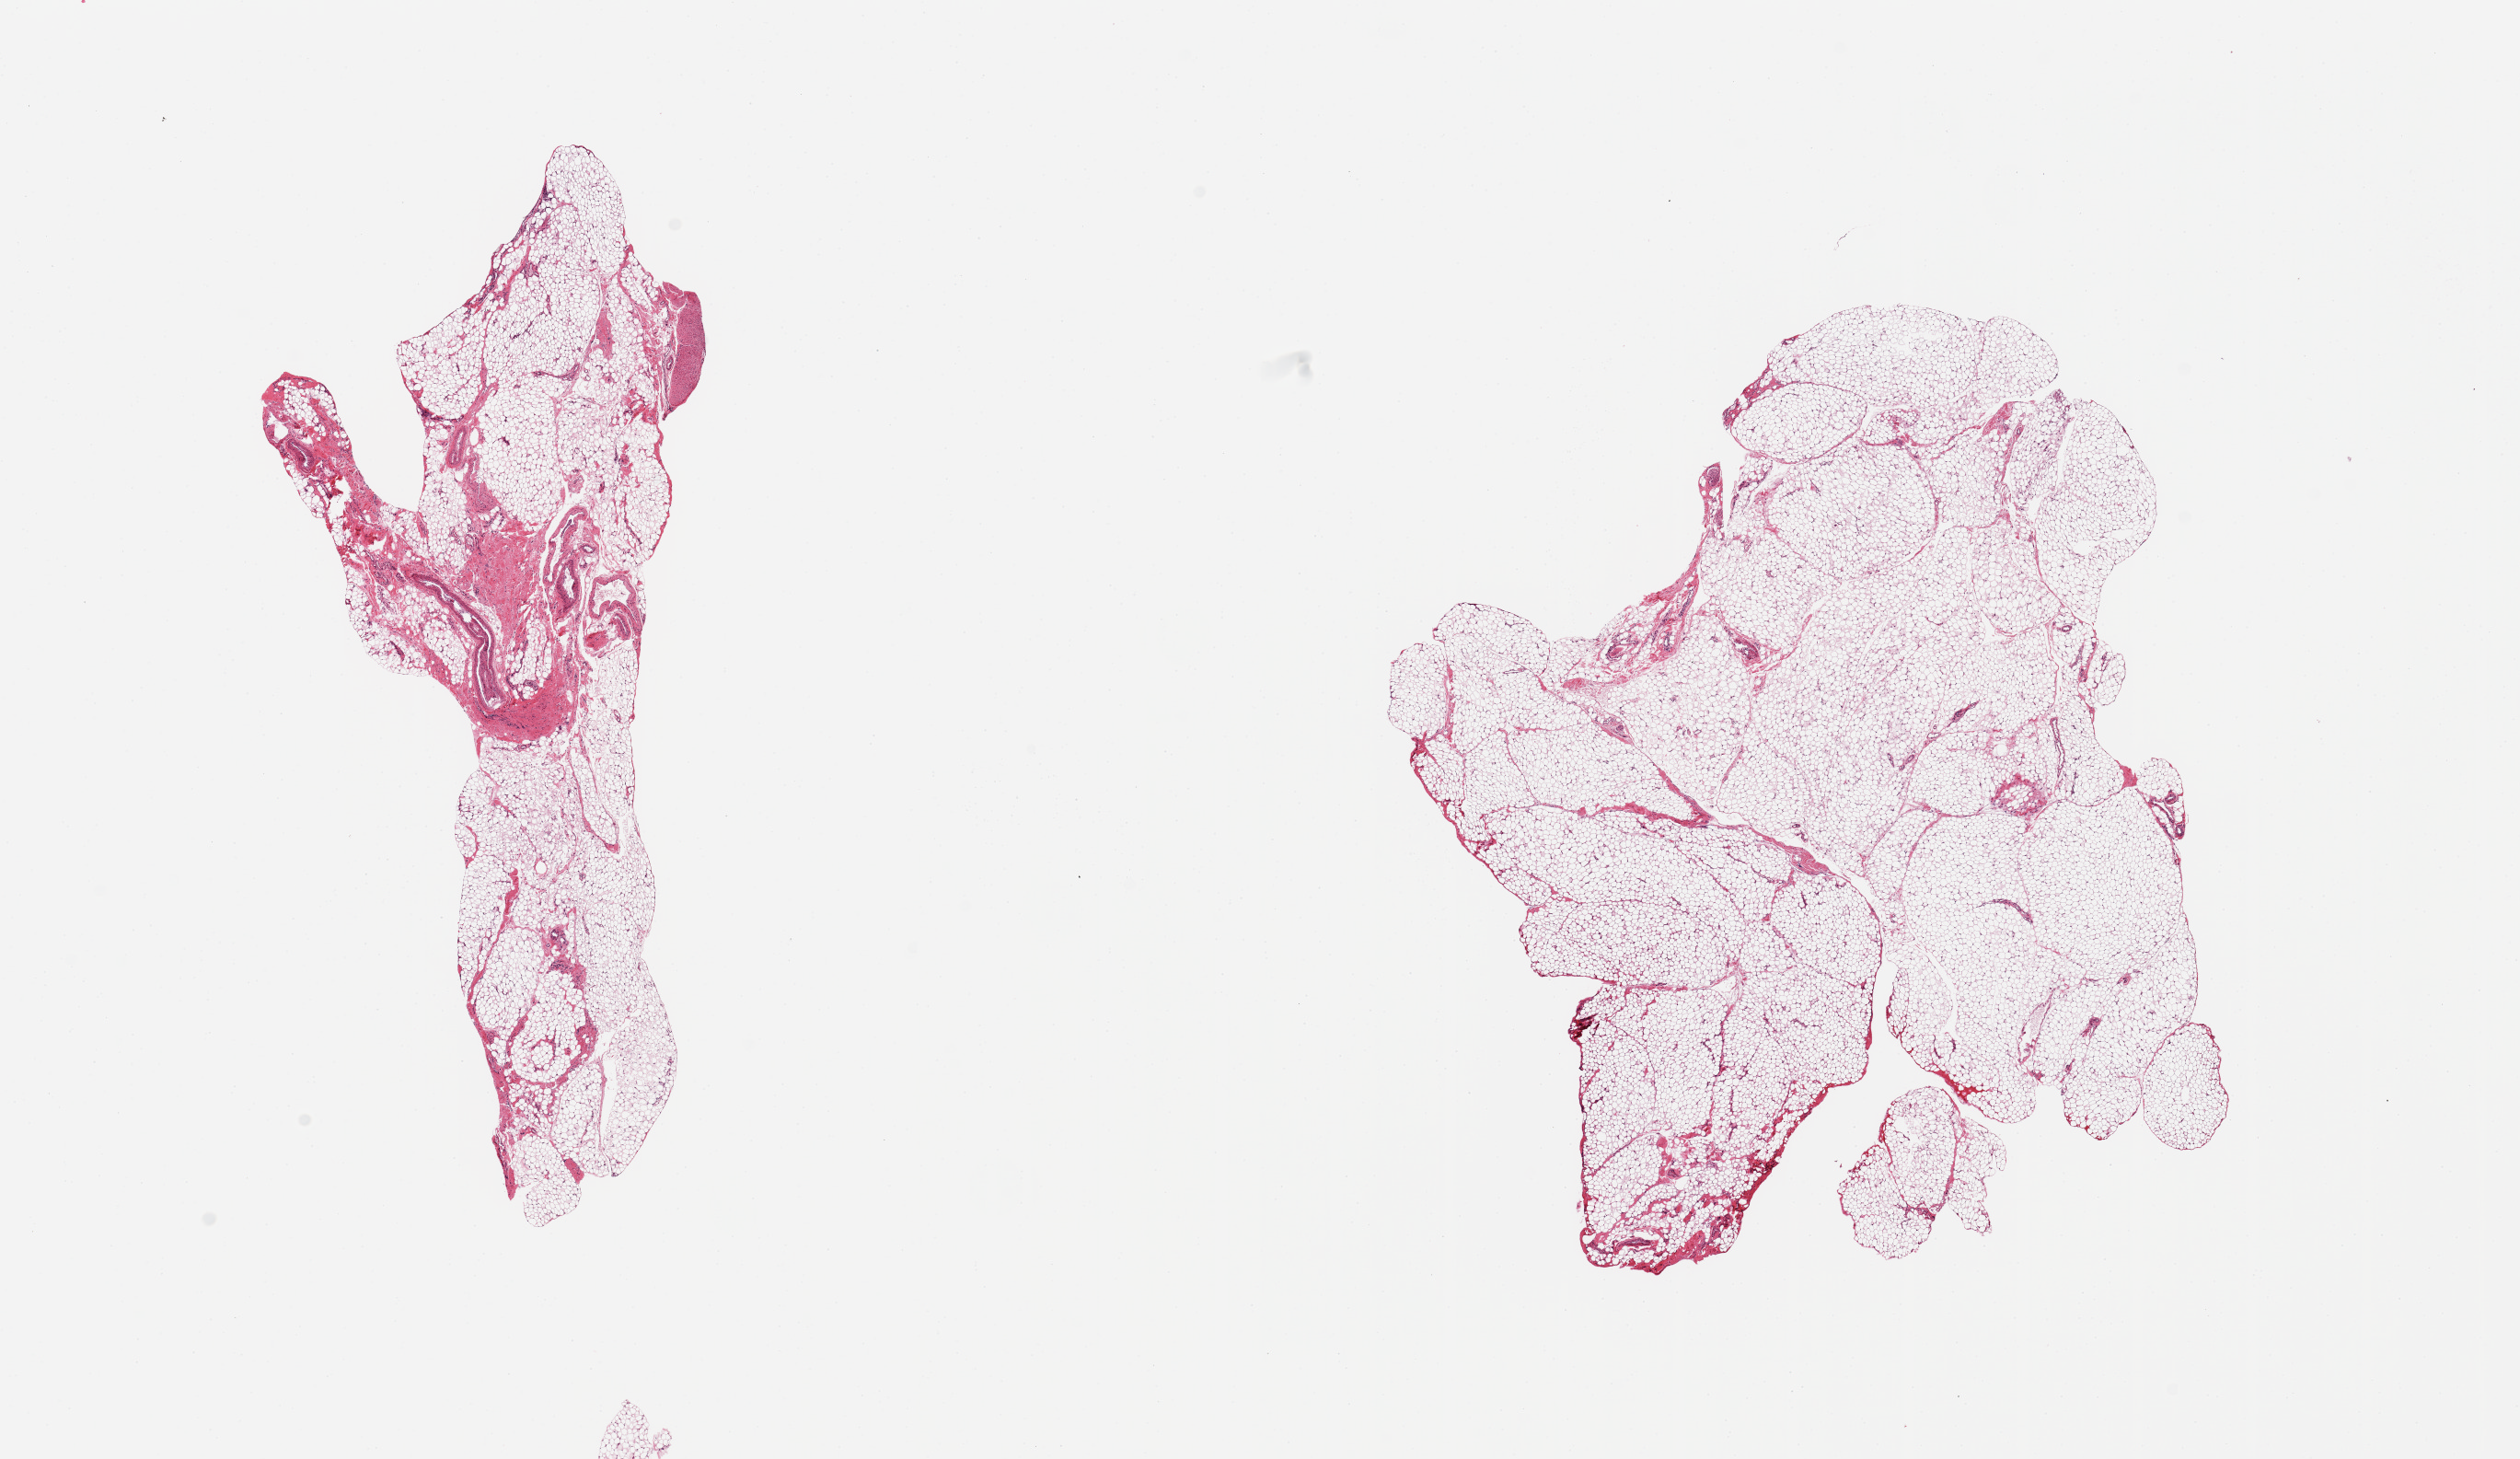
Whole-slide image, hematoxylin and eosin (H&E) stain, brightfield, low-resolution overview of the scanned area, about 21.7 x 12.5 mm (acquisition: 20x scan); PAXgene-fixed paraffin-embedded (PFPE) section; section of omentum (target tissue); tissue donor sample. Donor sex: female.
Pathologist's review note for this sample: 2 pieces, mesothelial fibrosis/fascia ~10% total.